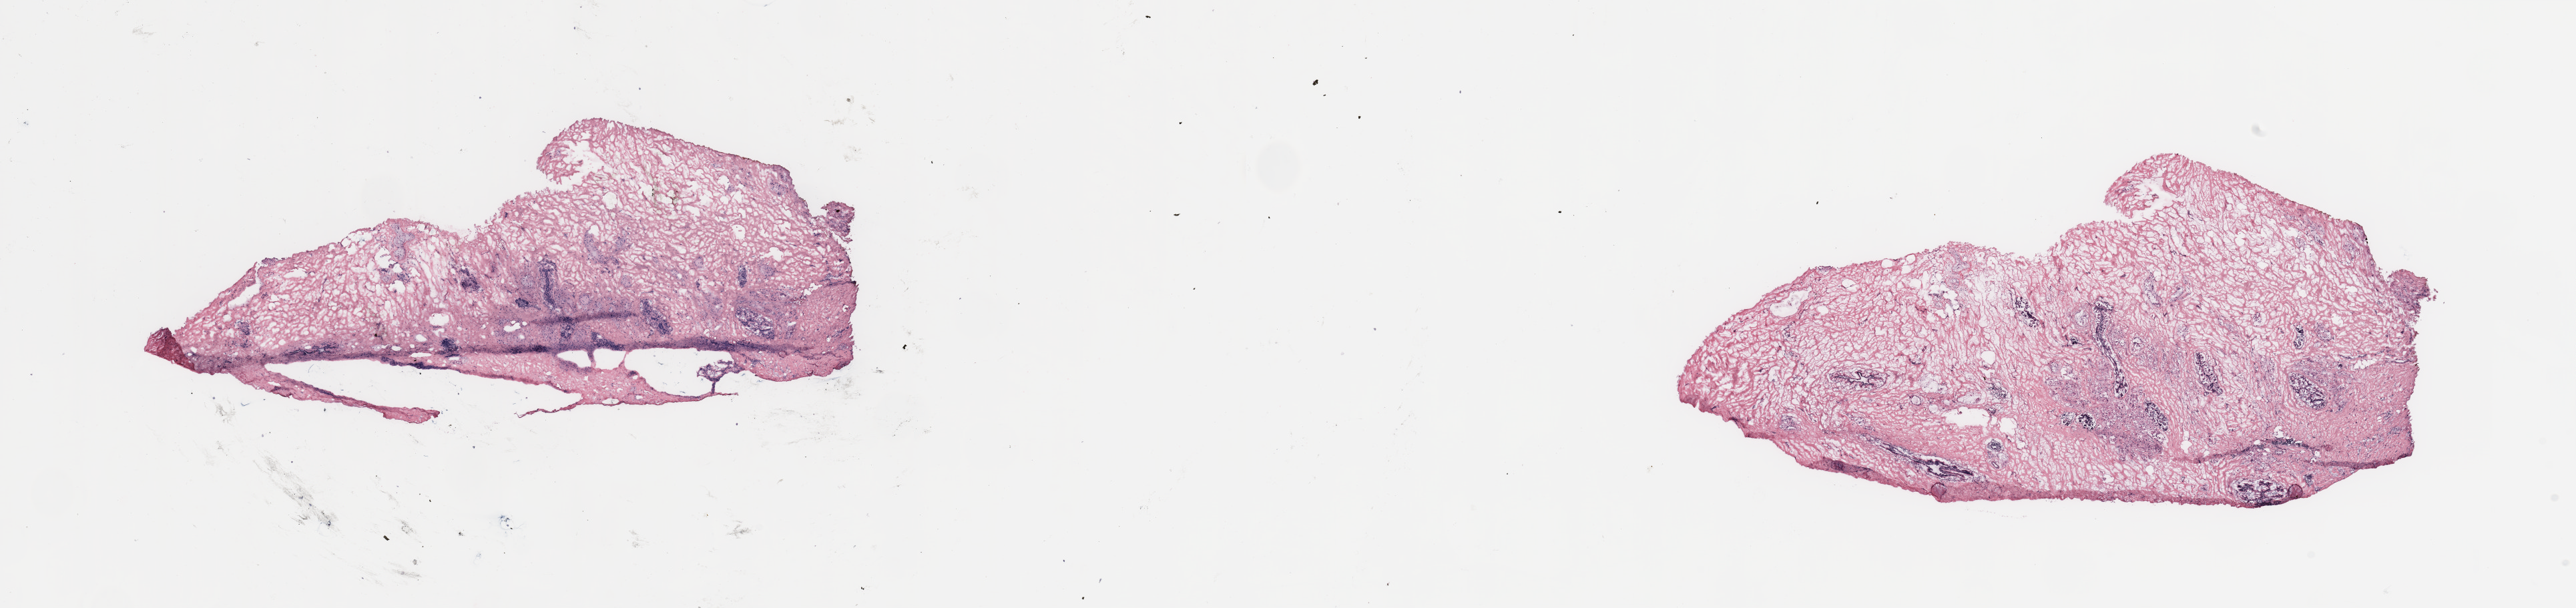
Digitized Hematoxylin and eosin (H&E) stained tissue section (whole slide) — a low-resolution overview of the entire scanned area, about 30.5 x 7.2 mm (slide scanned at 20x); breast, tissue type not recorded.
- patient diagnosis (cohort enrolment): breast cancer (breast)